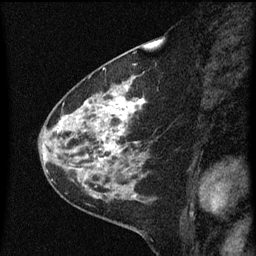
Breast MRI (dynamic contrast-enhanced), one sagittal slice; position 23 of 60 along the scan axis; dynamic contrast-enhanced series, image 2 of 3 at this slice position (ordered by acquisition); 1.5 T; TE 4.2 ms, TR 8 ms; 2 mm slice thickness; 256 × 256 image matrix. Female patient, age 60 years.
Structures marked on this image (semi-automatically segmented with operator editing):
- analysis volume of interest (the breast-tissue region the enhancement analysis was run in; not a lesion): bounding box <48,82,152,183> (left, top, right, bottom; pixels)
- tumour enhancement mask (voxels above the 70 % enhancement threshold inside the analysis volume of interest): <58,86,143,161>